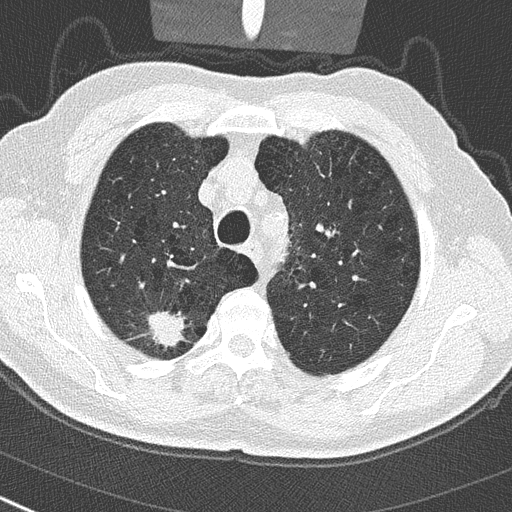
Low-dose screening chest CT, one axial slice; slice 230 of 290 in the series (ordered by position); 120 kVp; lung window (W 1500 / L -600 HU); 2 mm slice thickness; 512 × 512 image matrix, field of view 300 × 300 mm.
Annotated regions visible in this slice (outlined manually by an expert reader):
- lesion 1 (tumor, upper lobe of right lung): box from (x=147, y=311) to (x=186, y=350) px